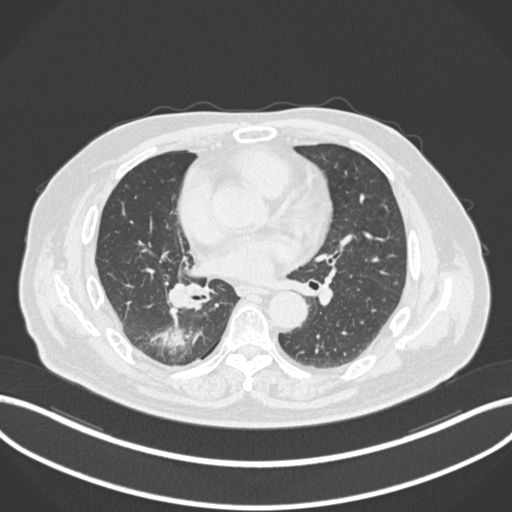
Chest CT, one axial slice; slice 90 of 218 in the series (ordered by position); 120 kVp; lung window (W 1500 / L -600 HU); 1 mm slice thickness; 512 × 512 image matrix, field of view 400 × 400 mm. Male patient, age 68 years. From the clinical record (not read from this slice): clinical TNM (as recorded): T2a N0 M0.
Structures marked on this image (rectangle marked by the reading radiologist):
- lung tumour (recorded histology: adenocarcinoma): bounding box <147,323,200,351> (left, top, right, bottom; pixels)